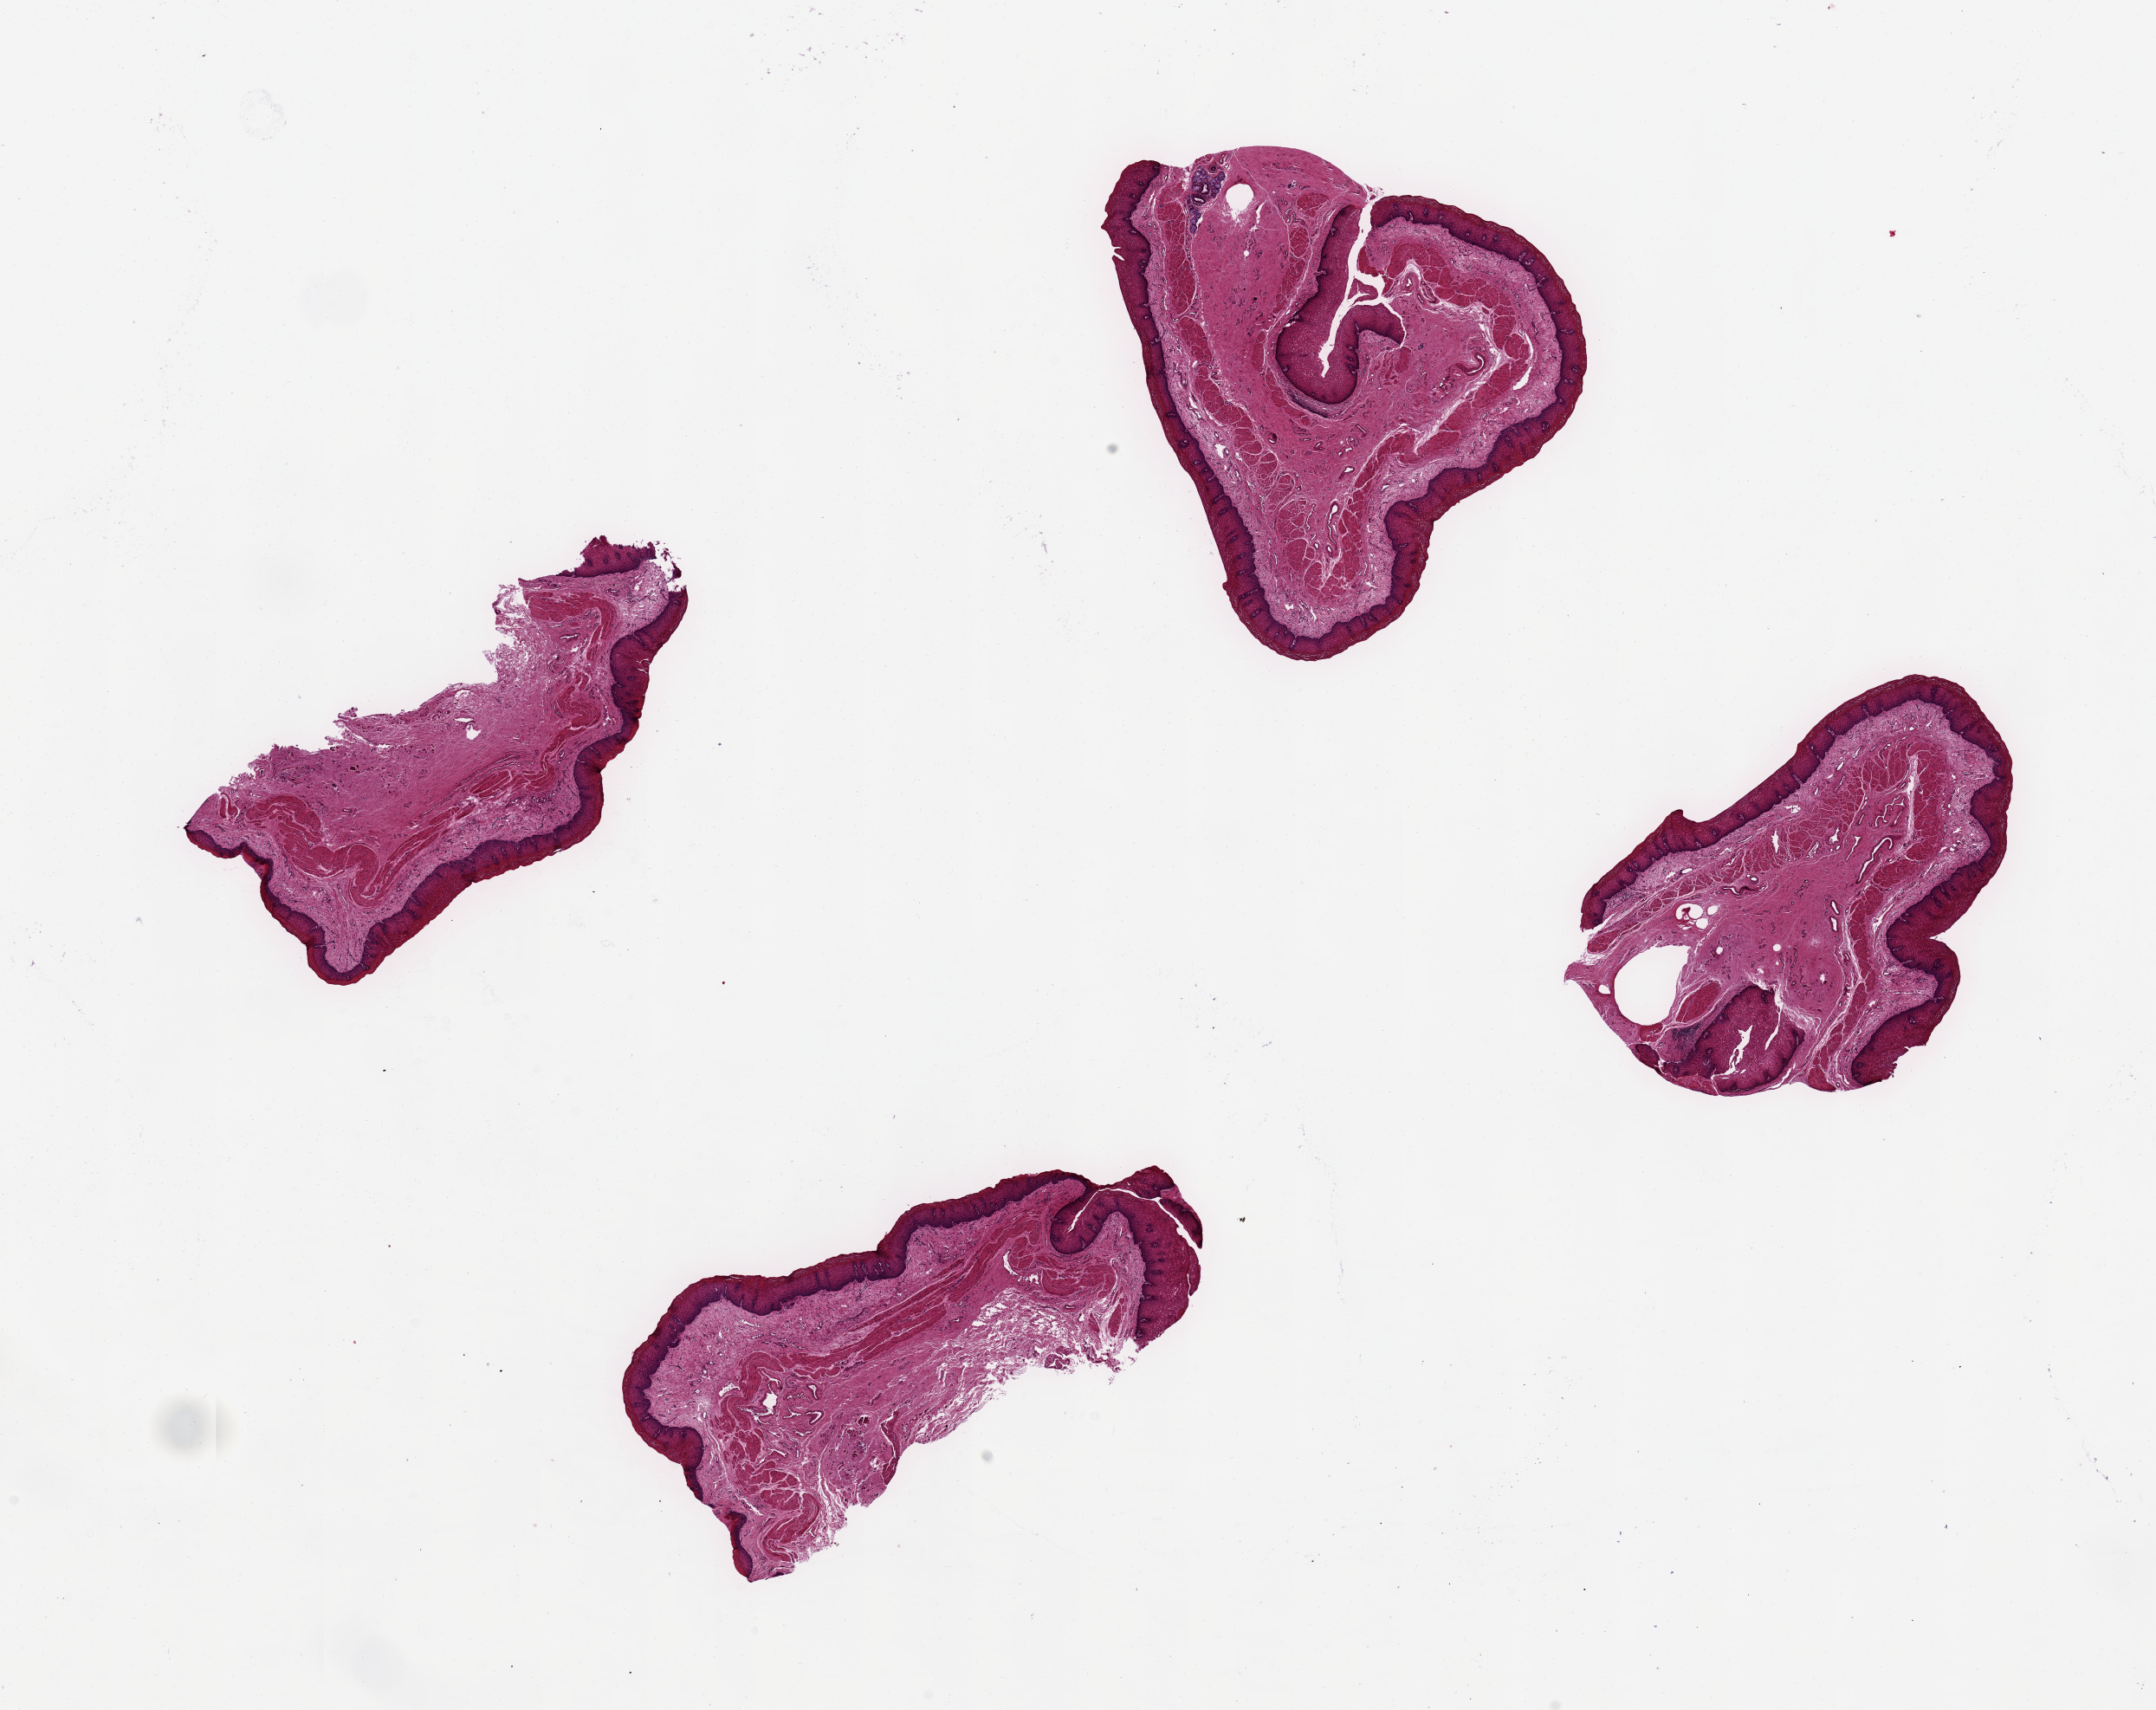
H&E whole-slide image, brightfield — a low-resolution overview of the entire scanned area, about 19.7 x 15.6 mm (slide scanned at 20x); PAXgene-fixed, paraffin-embedded tissue; section of esophageal mucous membrane (target tissue); donor tissue sample. Female donor.
Reviewer comment on this tissue sample: 4 pieces, ~4x4mm; mucosa=~0.3mm thick. Well preserved mucosa.